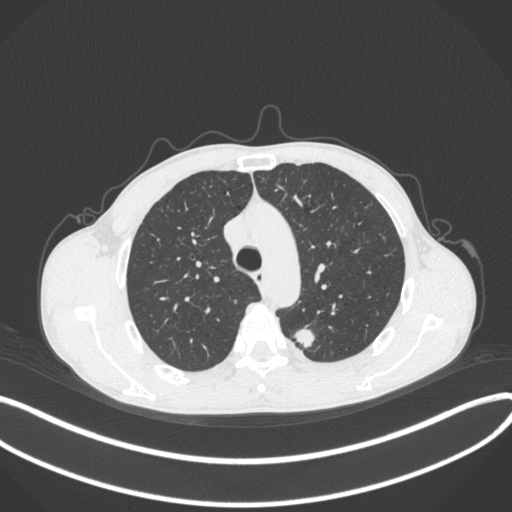
Chest CT, one axial slice; lung window (W 1500 / L -600 HU); 1 mm slice thickness; 512 × 512 image matrix, field of view 400 × 400 mm. Male patient, age 51 years. From the clinical record (not read from this slice): clinical TNM (as recorded): T2a N1 M1.
Outlined on this slice (bounding box drawn by a radiologist):
- lung tumour (recorded histology: adenocarcinoma): box from (x=291, y=324) to (x=319, y=355) px